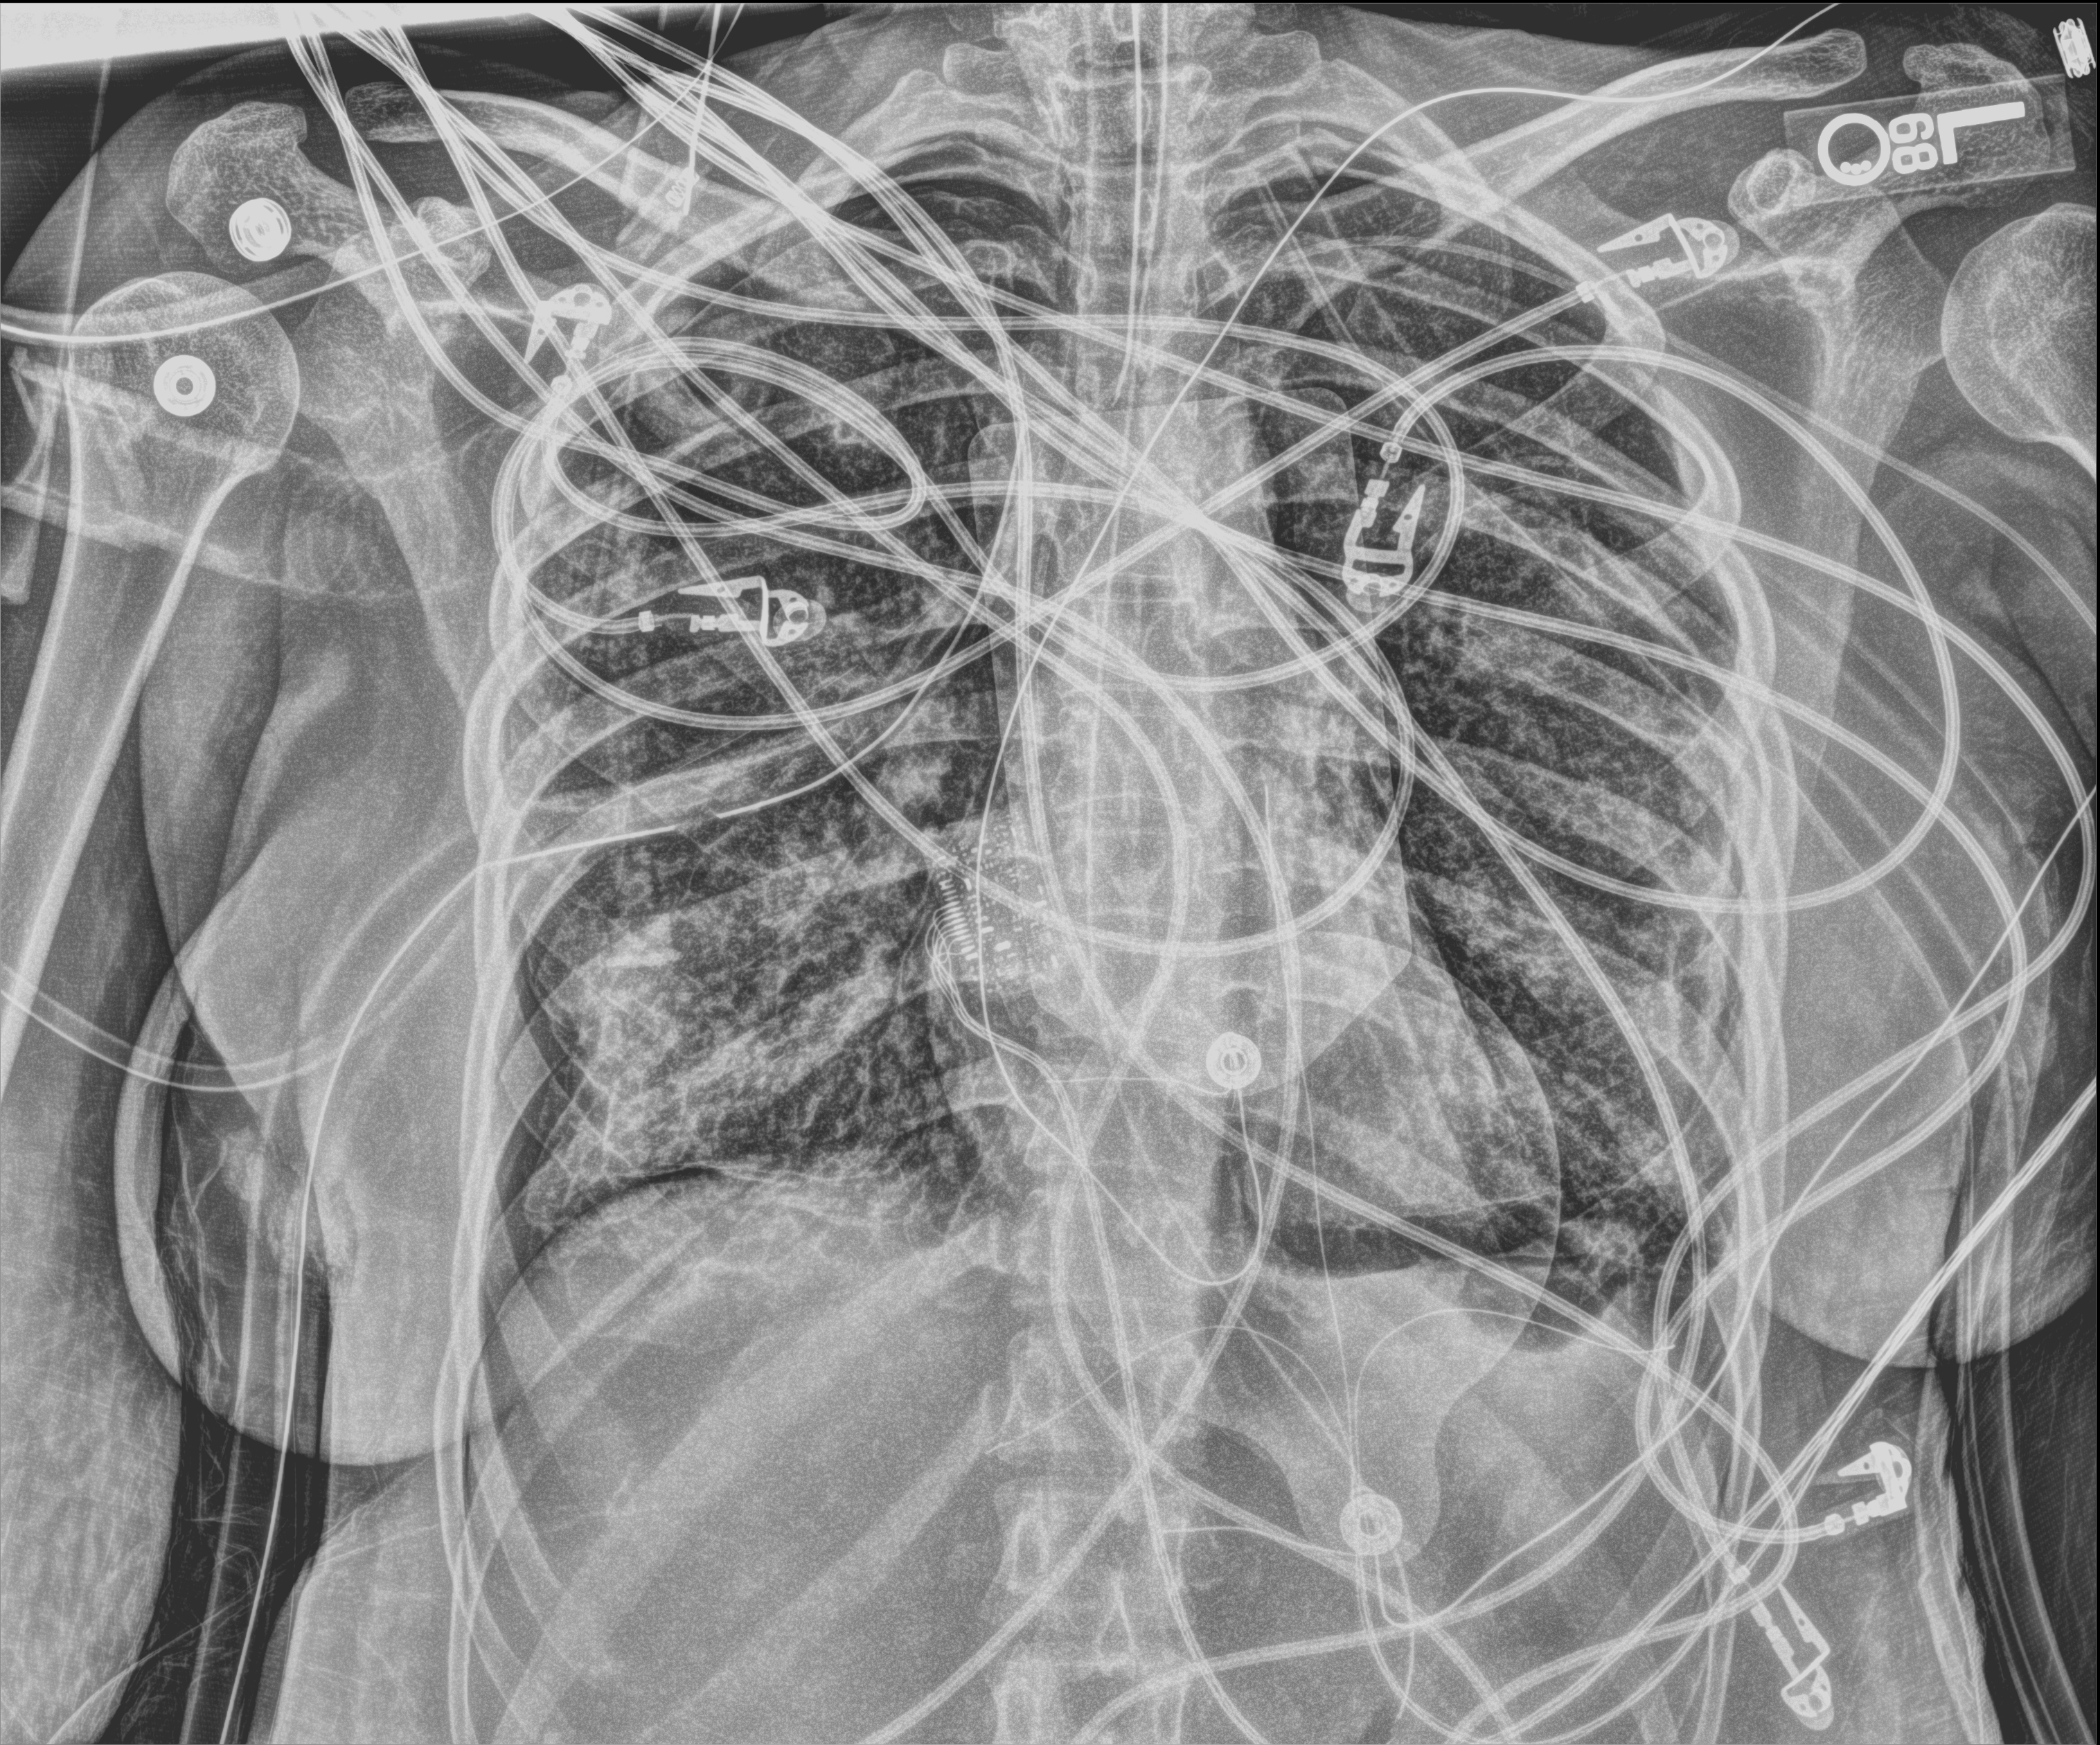
Bedside chest radiograph (digital radiography); anteroposterior (AP) projection. Patient hospitalised with COVID-19, aged 18–59 years.
Hospital-stay facts (about this admission, not read from this image; timing relative to this image not recorded):
- admitted to intensive care during this hospital stay: yes
- hypertension (admission record): no